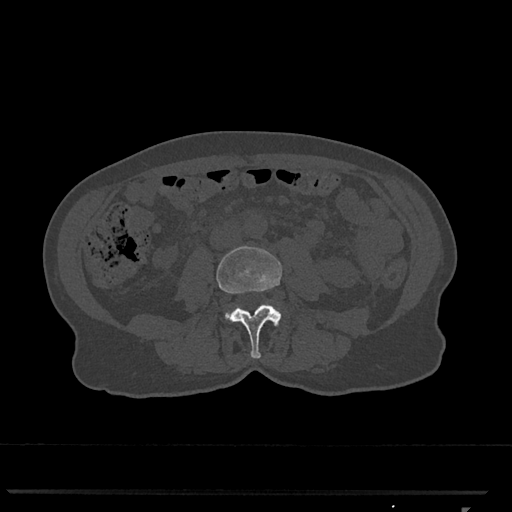
CT including the spine, one axial slice. Slice 257 of 793 in the series (ordered by position). 120 kVp. Bone window (W 1800 / L 400 HU). 0.5 mm slice thickness. 512 × 512 image matrix, field of view 380 × 380 mm. Patient: female, 62 years. Case-level facts recorded for this patient, not image findings: primary cancer: renal.
Structures marked on this image (semi-automatically segmented with operator editing):
- L3 vertebra: bounding box (x1, y1, x2, y2) in pixels: (217, 246, 282, 359)